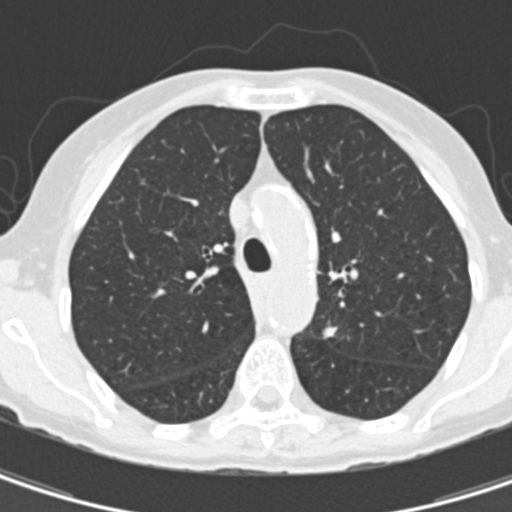
Axial slice from a low-dose chest CT screening exam, baseline screening round, lung window (W 1500 / L -600 HU), slice 50 of 157 in the series, 512 × 512 image matrix, field of view 260 × 260 mm. Female participant, aged 67 years at enrolment. Current smoker at enrolment.
Expert reader's lesion annotation, bounding box (x1, y1, x2, y2) in pixels: (315, 314, 358, 361). The exam's reader record, not a measurement of the box and not confirmed to be the same lesion: non-calcified nodule or mass ≥4 mm, left upper lobe, 11 × 8 mm, spiculated (stellate) margins, soft tissue attenuation. Participant outcome: lung cancer diagnosed 73 days after this screen — adenocarcinoma, NOS, left upper lobe, poorly differentiated (G3), stage IA (AJCC 6th edition), 13 mm at pathology.